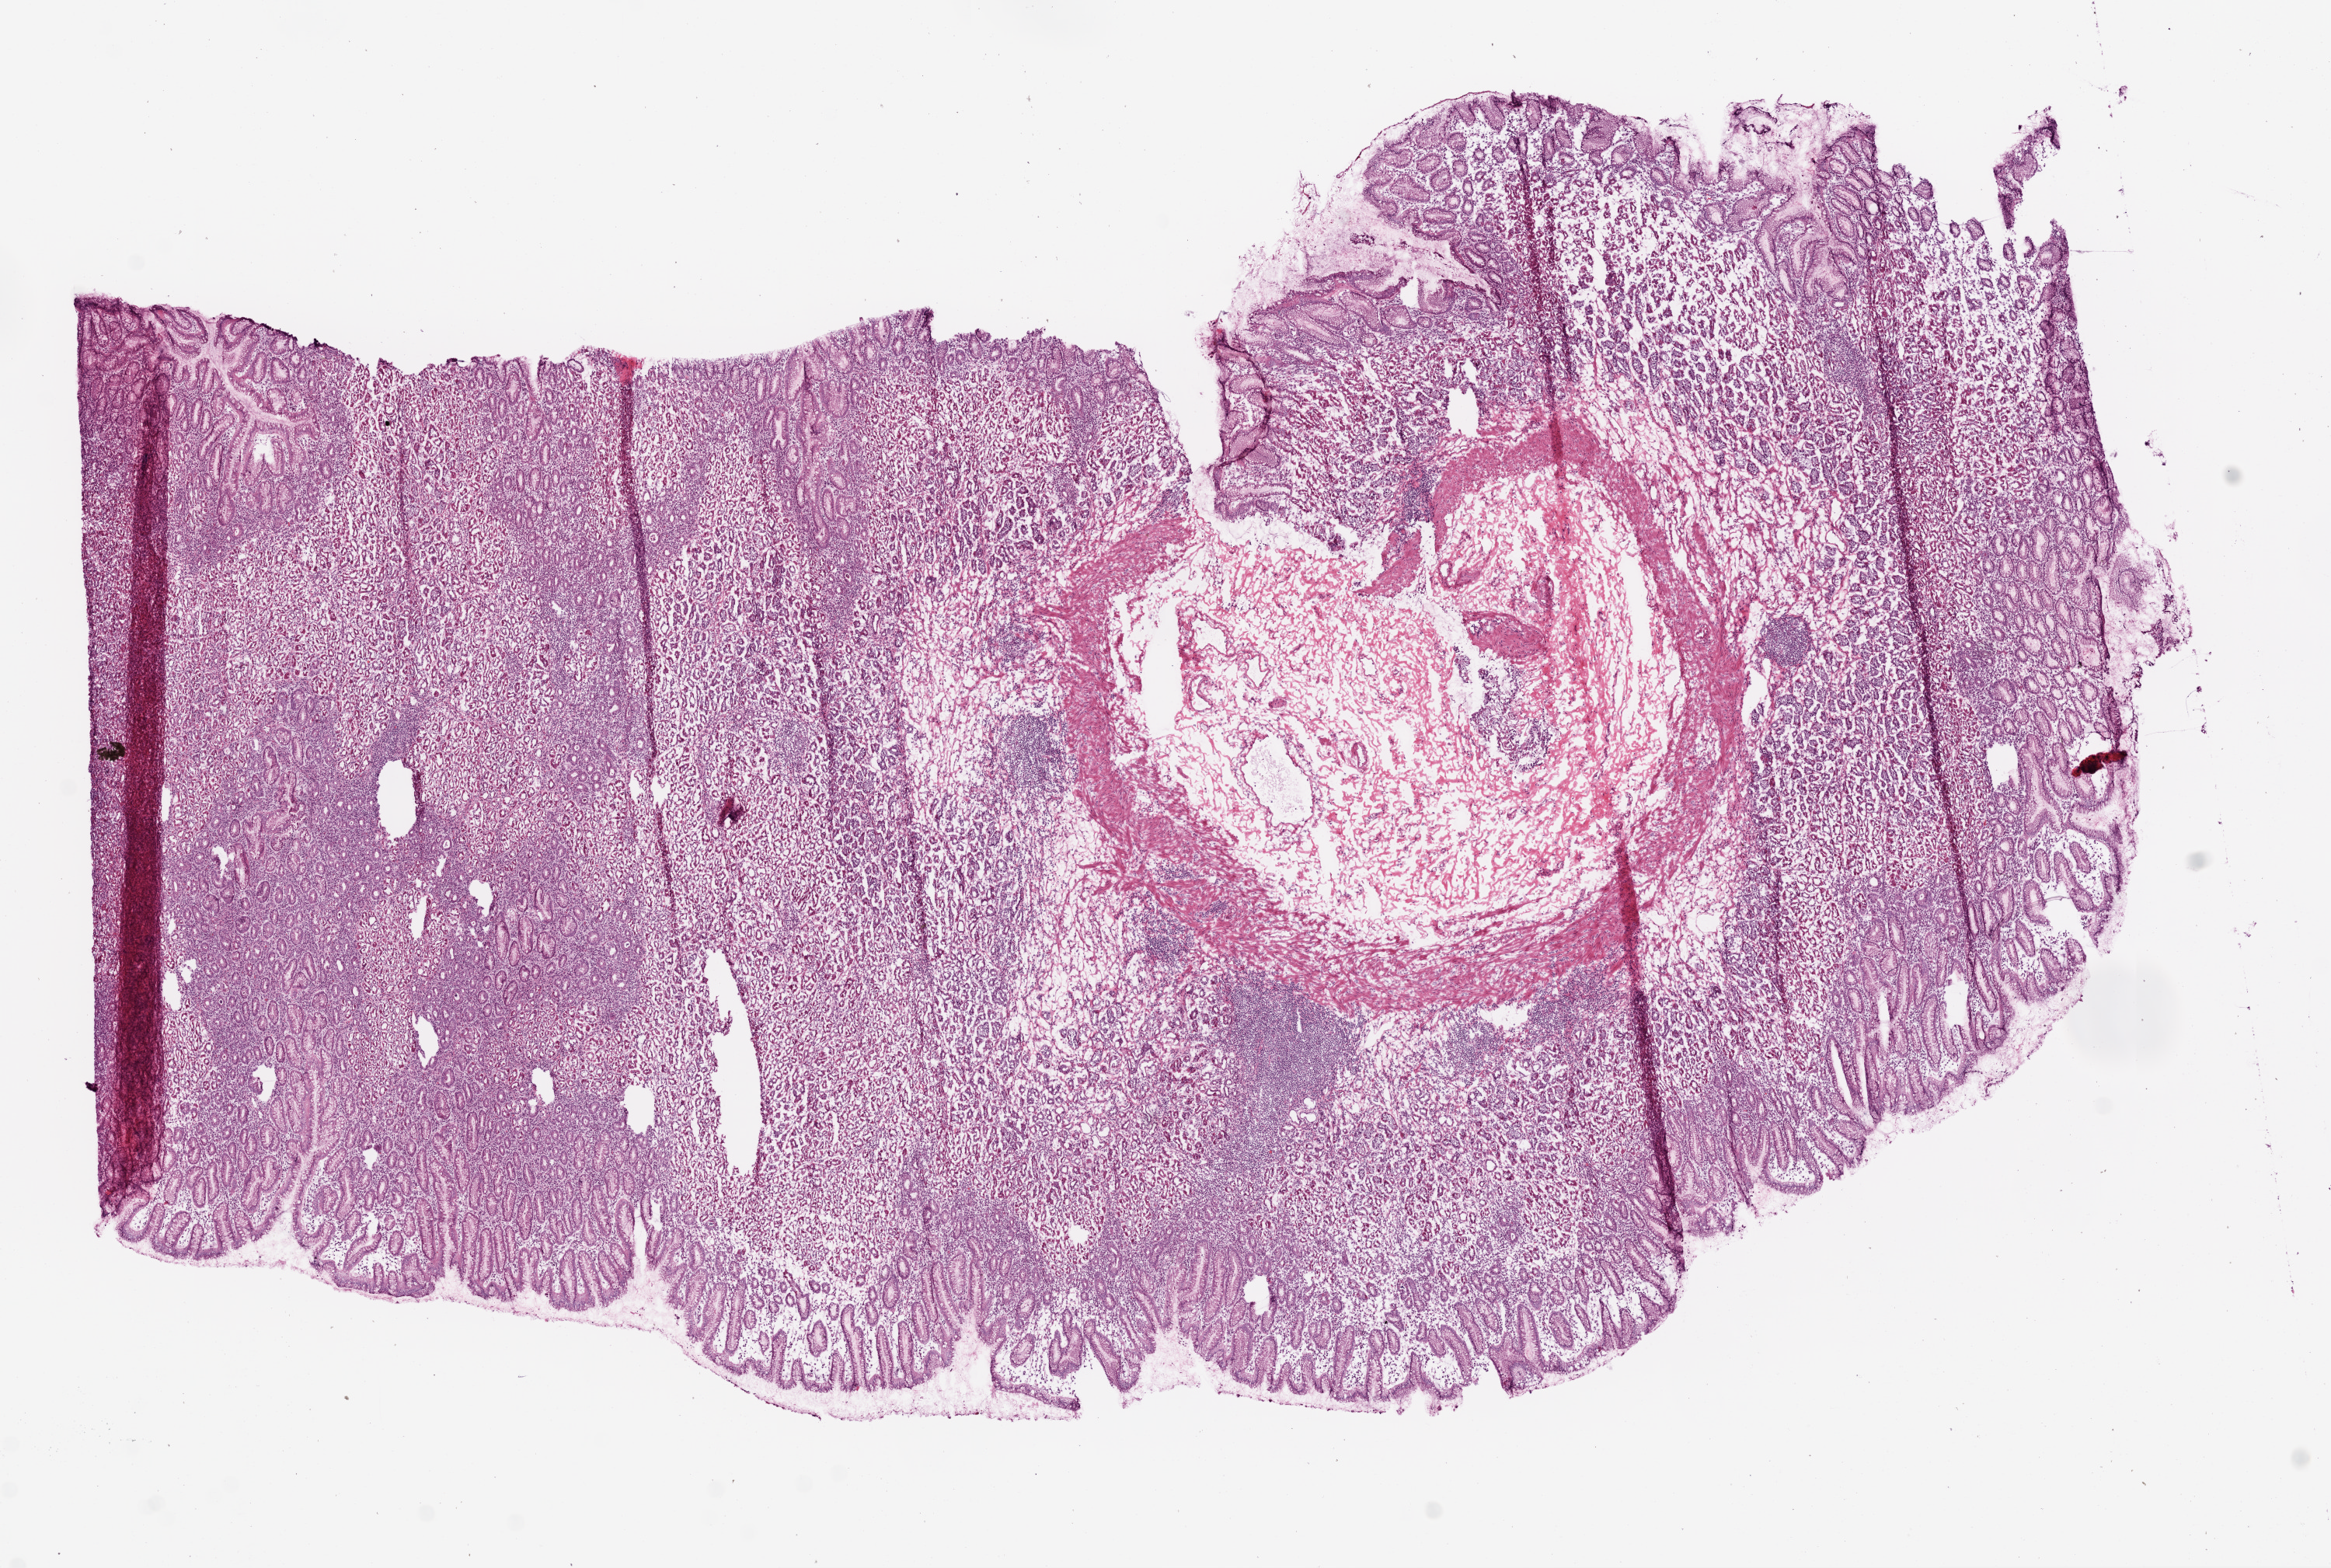
Digitized H&E tissue section (whole slide), shown as a low-resolution overview of the whole scanned area (about 12.0 x 8.1 mm); frozen section; sample: solid tissue normal (non-tumour tissue), stomach. Patient: male, age at initial diagnosis 65 years.
This section: solid tissue normal sample (biorepository sample class). Patient diagnosis: Tubular adenocarcinoma (body of stomach).